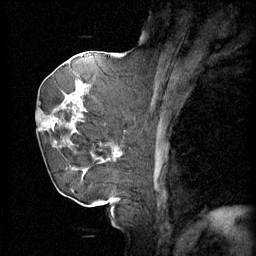
Breast MRI (dynamic contrast-enhanced), one sagittal slice; position 26 of 60 along the scan axis; 4 images stored at this slice position (order not interpretable as contrast timing); 1.5 T; TE 4.2 ms, TR 11 ms; 2 mm slice thickness; 256 × 256 image matrix. Female patient, age 72 years.
Outlined on this slice (semi-automatic segmentation, software-assisted and operator-edited):
- analysis volume of interest (the breast-tissue region the enhancement analysis was run in; not a lesion): bounding box (x1, y1, x2, y2) in pixels: (43, 68, 109, 163)
- tumour enhancement mask (voxels above the 70 % enhancement threshold inside the analysis volume of interest): (43, 72, 109, 163)